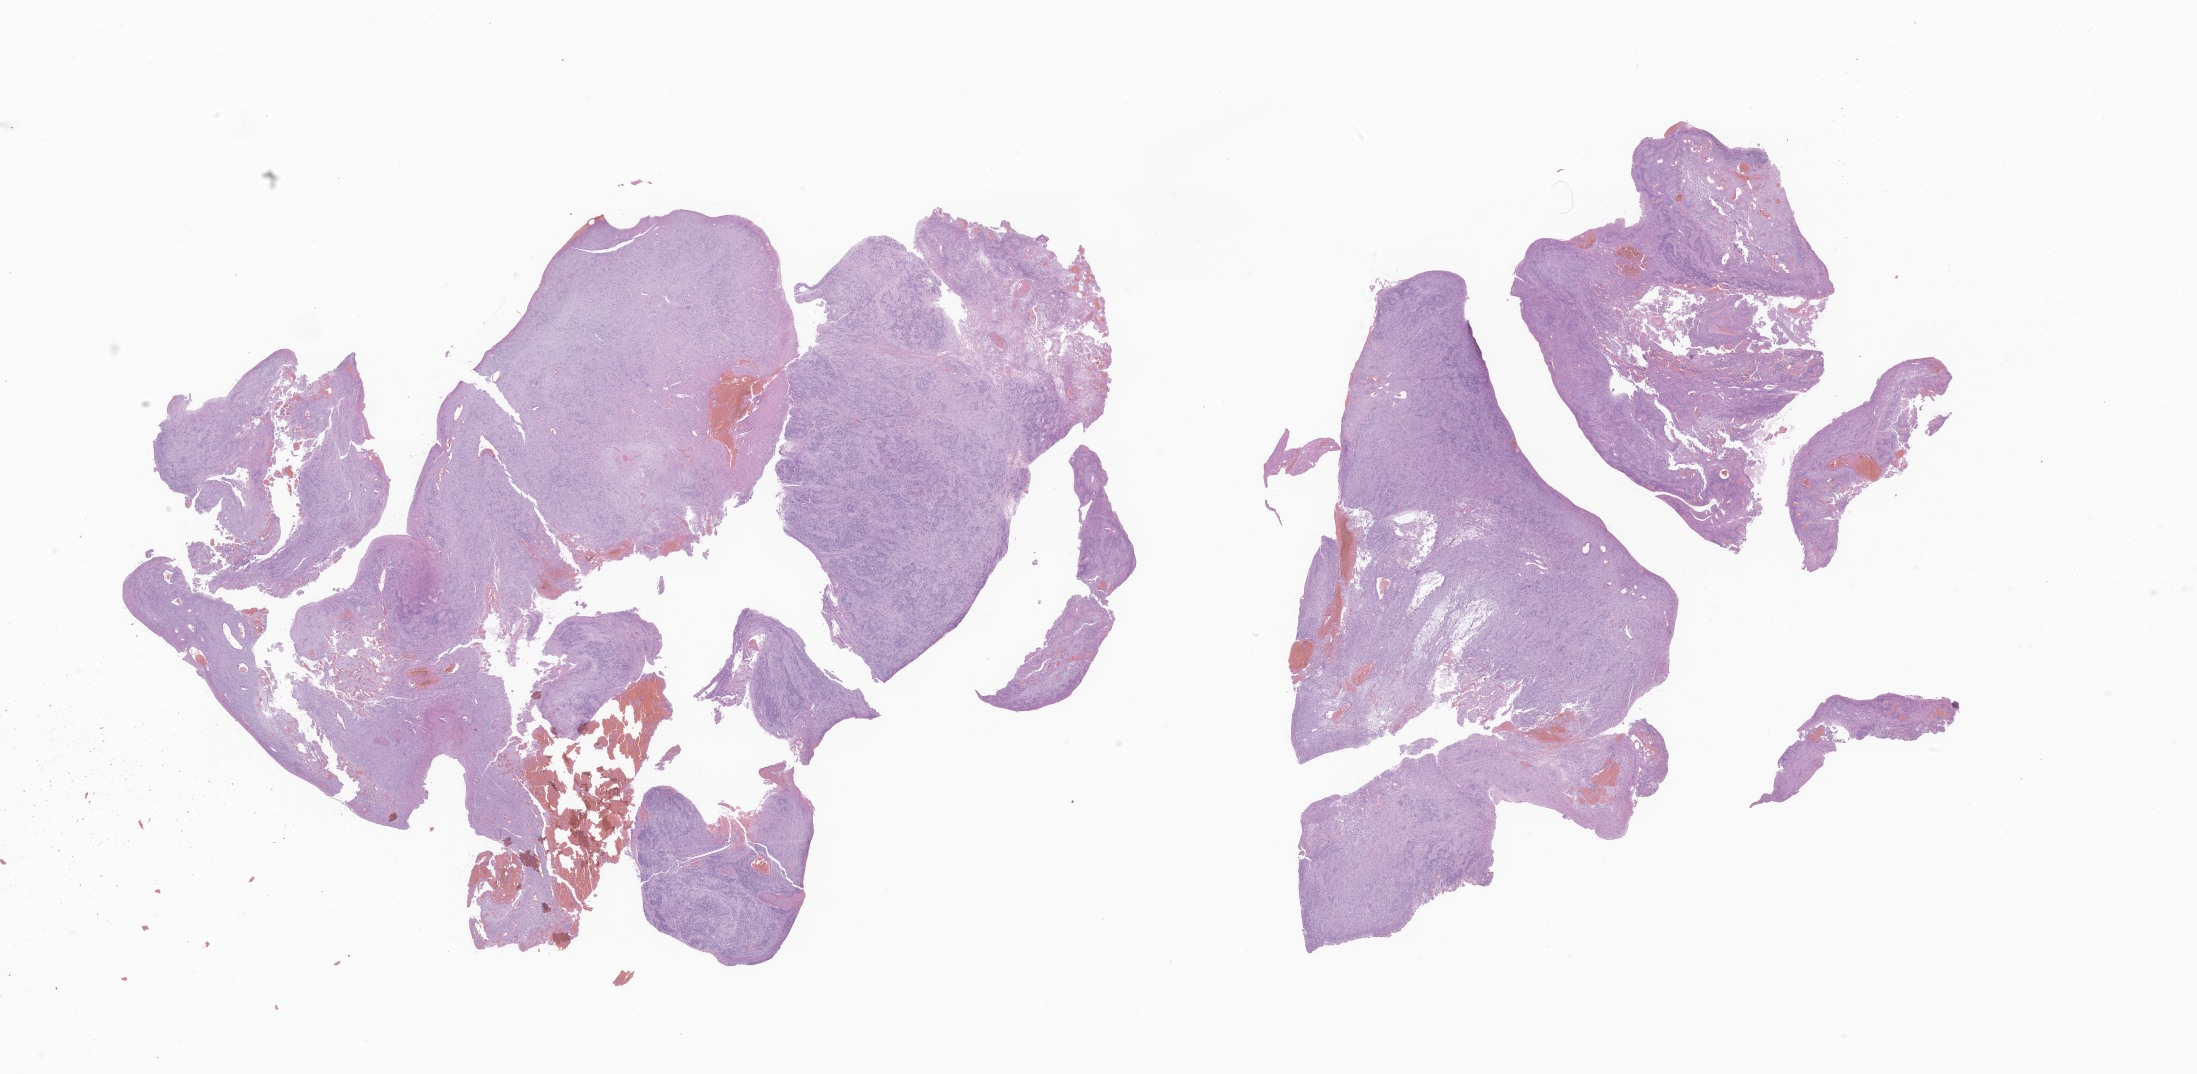
Hematoxylin and eosin (H&E) whole-slide image of tumor tissue from the brain, low-resolution overview of the scanned area, about 37.1 x 18.1 mm, FFPE section. Patient female; age 287 days.
Diagnosis: Ependymoma, NOS.